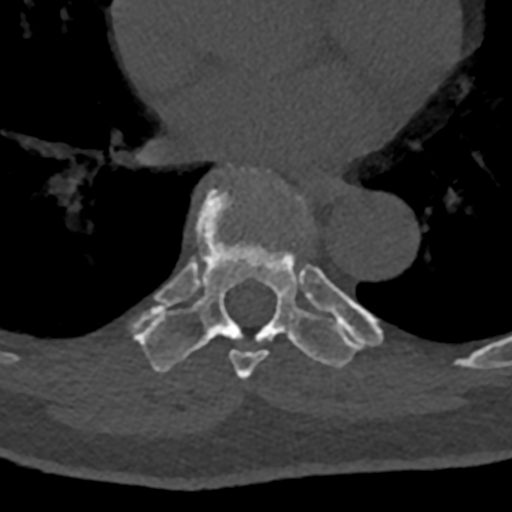
CT including the spine, one axial slice. Slice 728 of 797 in the series (ordered by position). Reconstruction kernel Br40s/3. 120 kVp. Bone window (W 1800 / L 400 HU). 512 × 512 image matrix, field of view 160 × 160 mm. Male patient, age 74 years. From the clinical record (not read from this slice): primary cancer: renal.
Annotated regions visible in this slice (semi-automatically segmented with operator editing):
- T7 vertebra: bounding box [x1, y1, x2, y2] px = [211, 167, 352, 380]
- T8 vertebra: [133, 165, 381, 372]